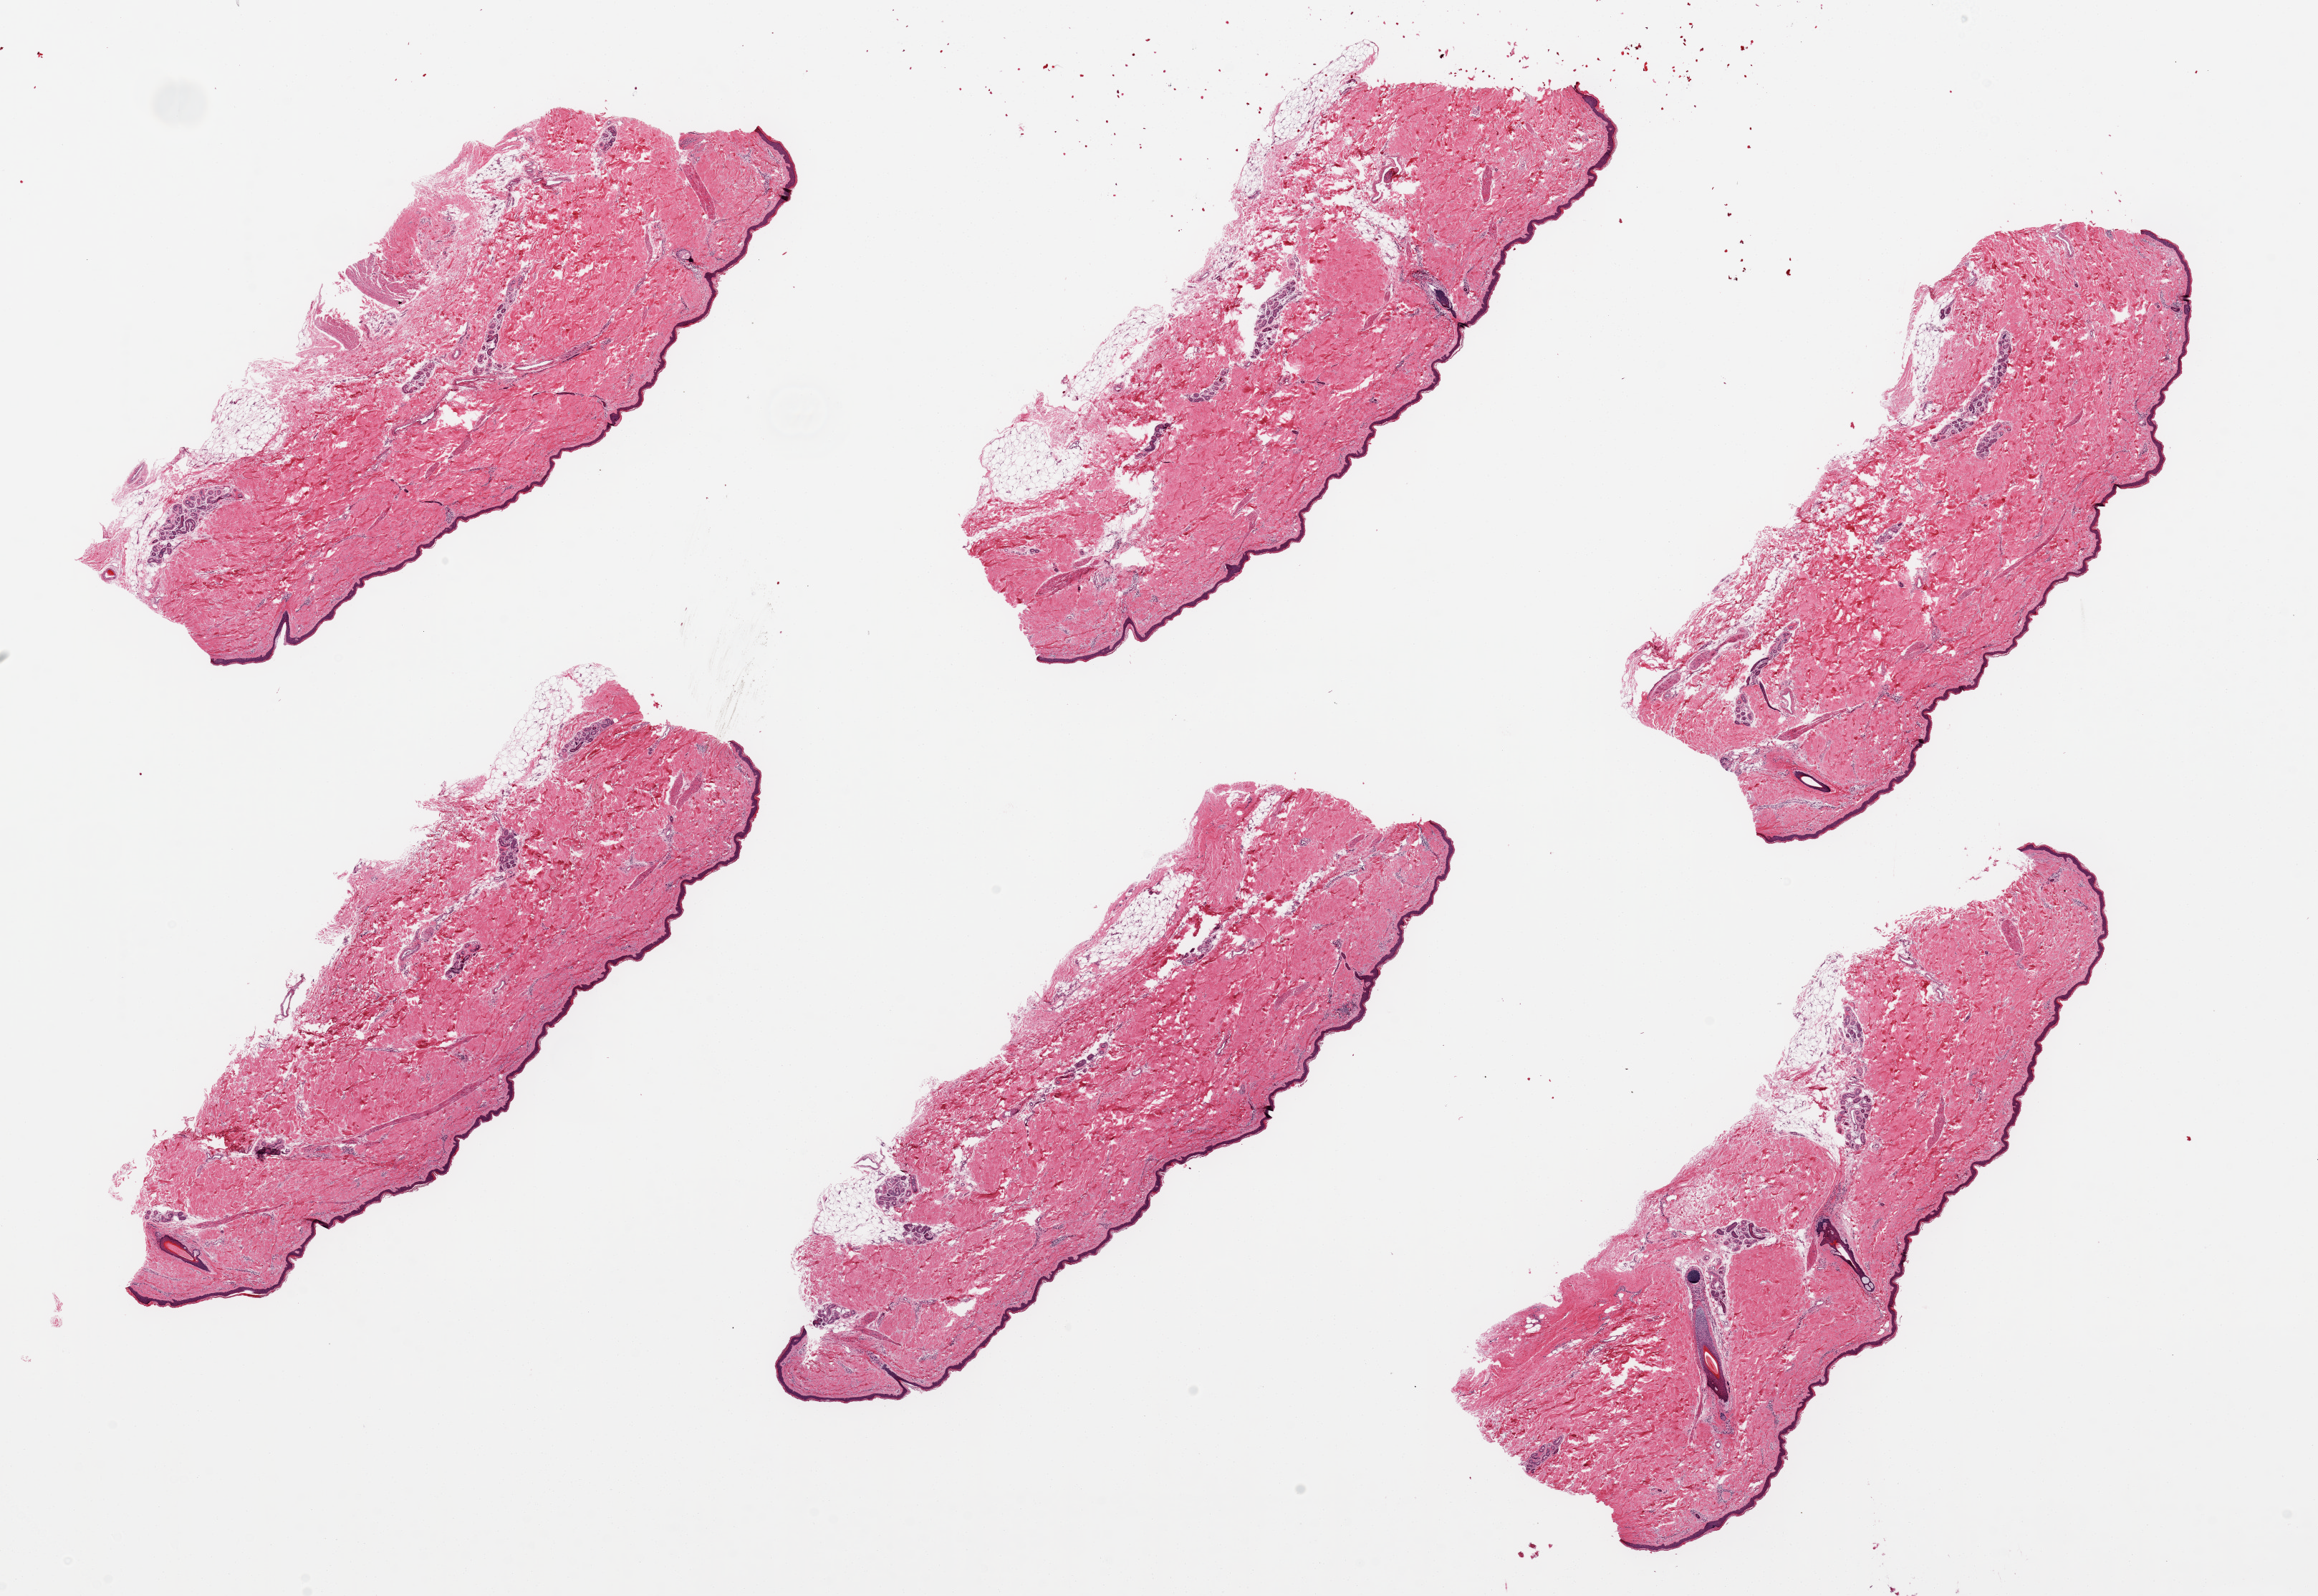
Whole-slide image, H&E stain, brightfield — a low-resolution overview of the entire scanned area, about 25.6 x 17.6 mm (acquisition: 20x scan), PAXgene-fixed, paraffin-embedded tissue, target tissue: skin of lower leg, donor tissue sample. Male donor.
Pathologist's review note for this sample: 6 pieces up to 9x3 mm.